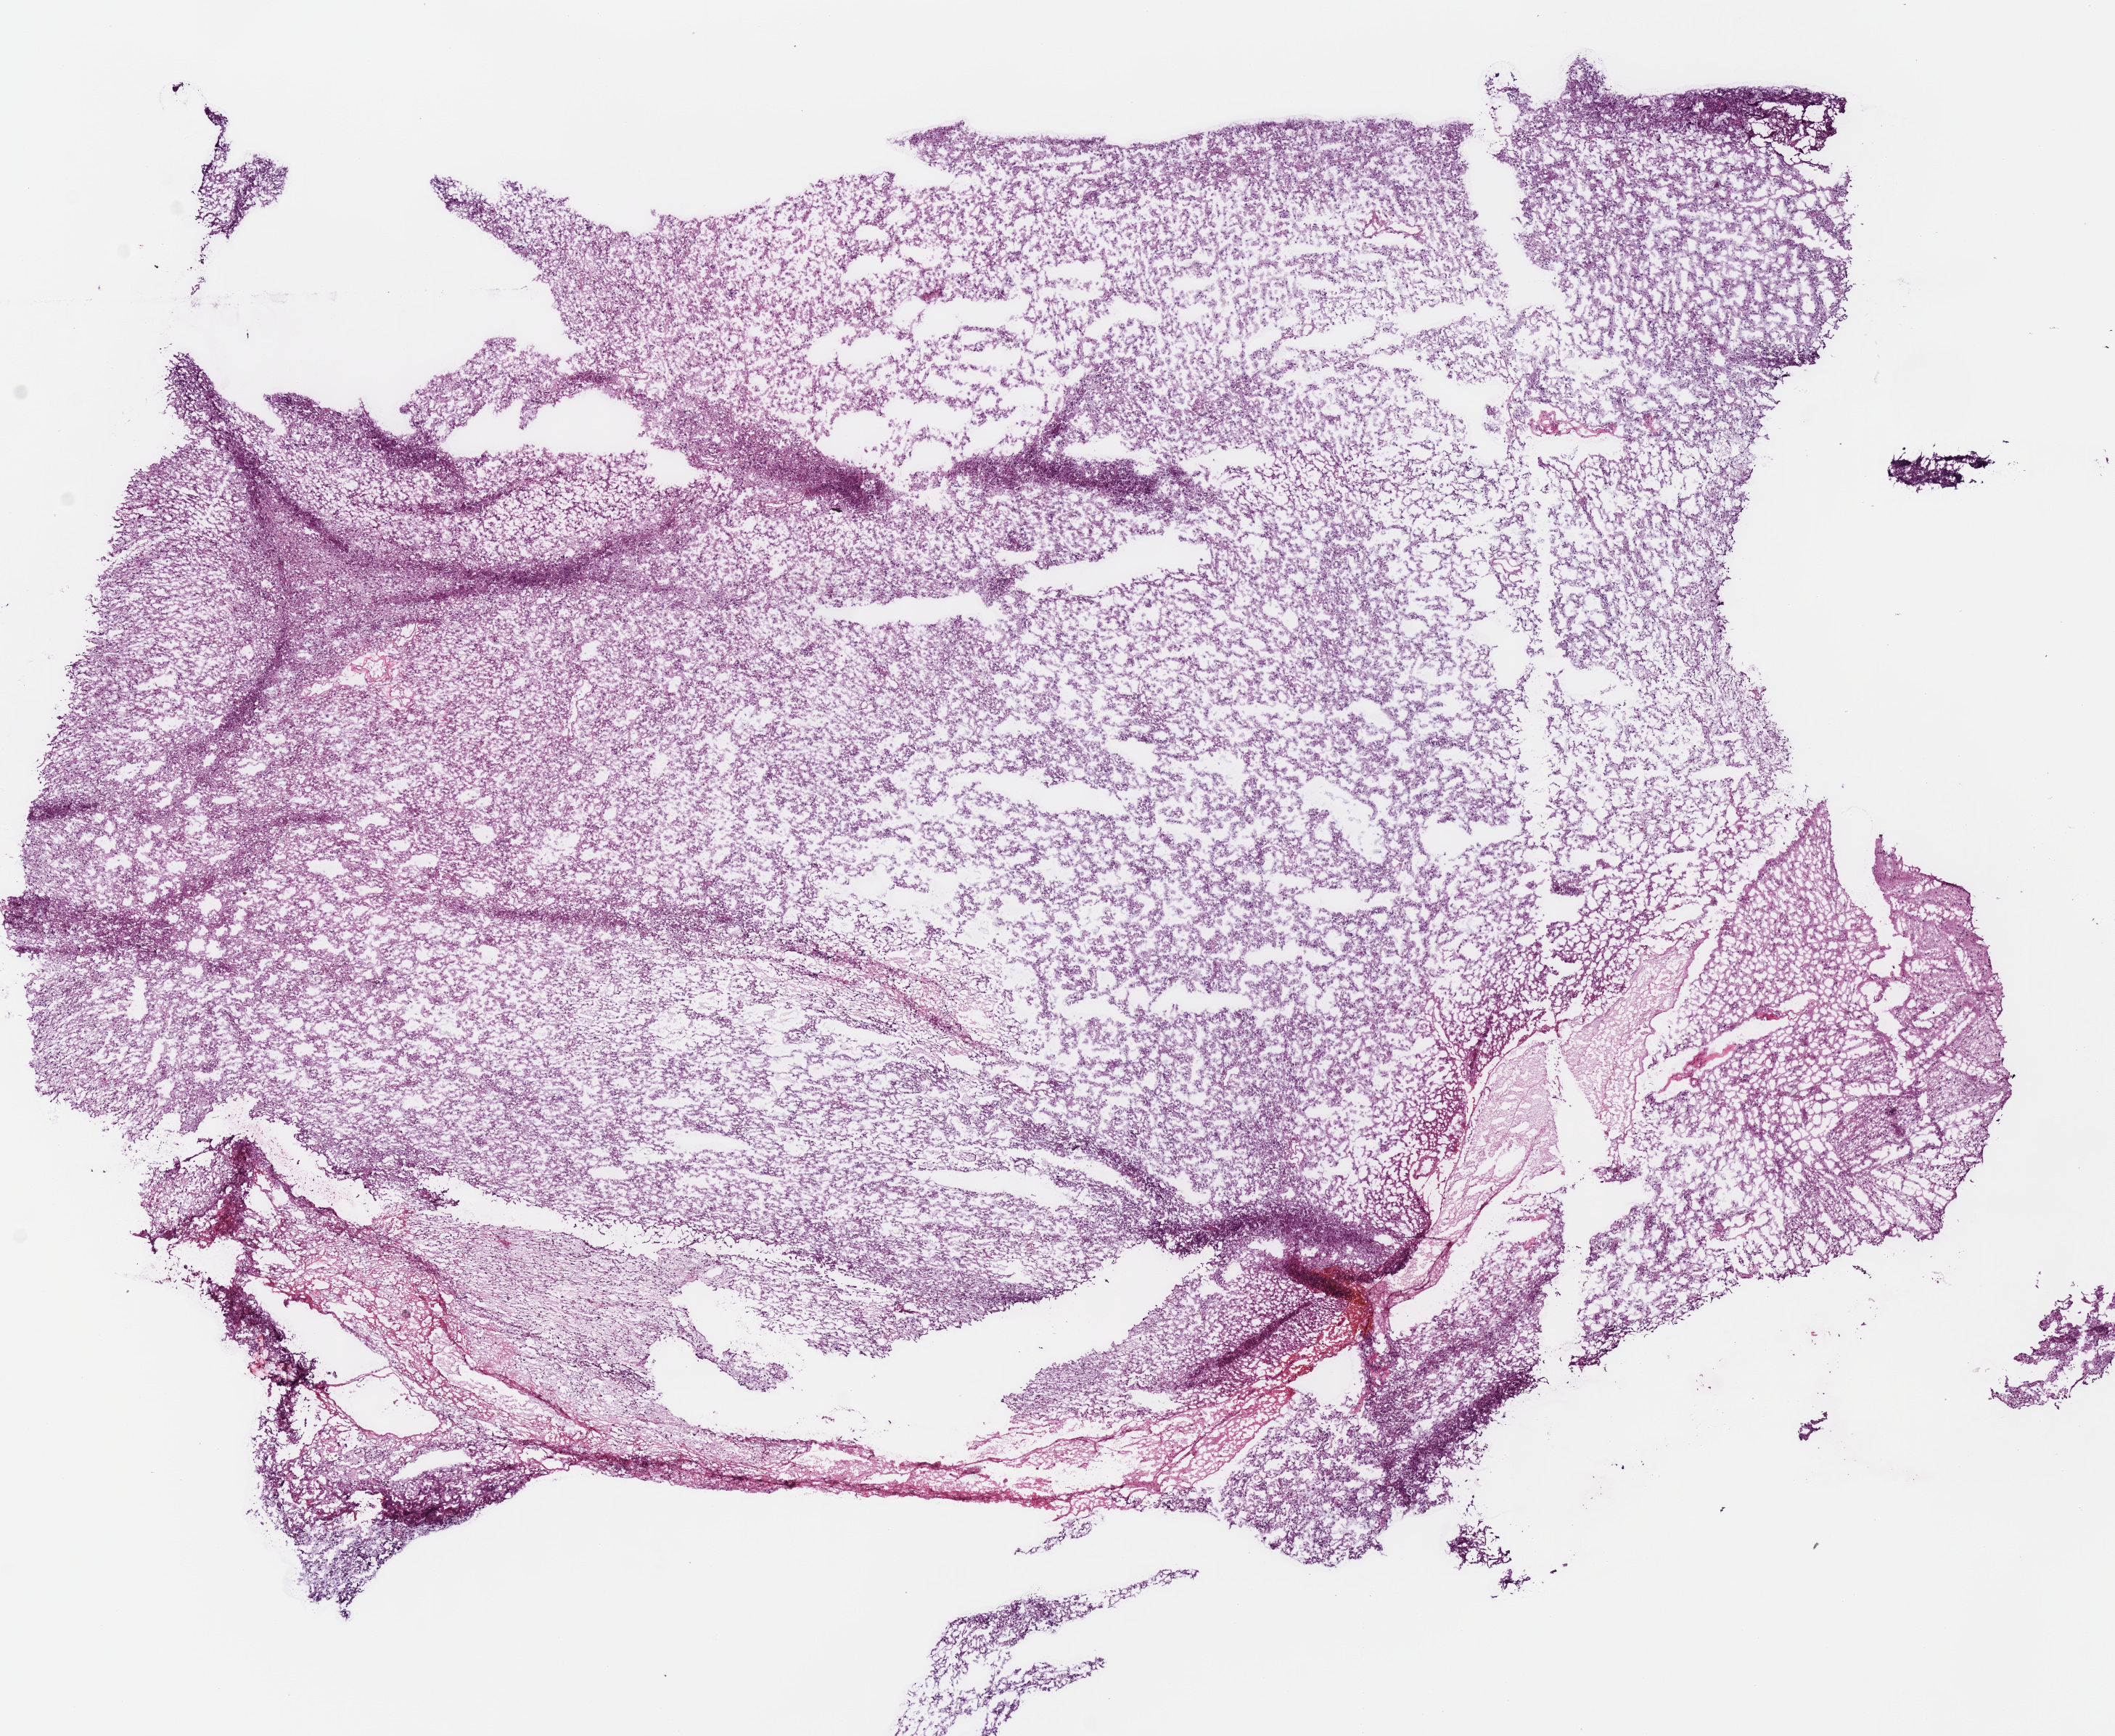
Digitized H&E-stained tissue section (whole slide), low-resolution overview of the scanned area, about 11.5 x 9.4 mm (acquisition: 40x scan). Frozen section from the bottom of the tissue portion. Brain, primary tumour sample. Patient: male, age at initial diagnosis 41 years. Histologic grade: G2 (moderately differentiated). Pathologist review of this section (percent, as recorded): tumour cells 100%, tumour nuclei 75%, normal cells 0%, stromal cells 0%, necrosis 0%.
Pathologic diagnosis: Astrocytoma, NOS (cerebrum).